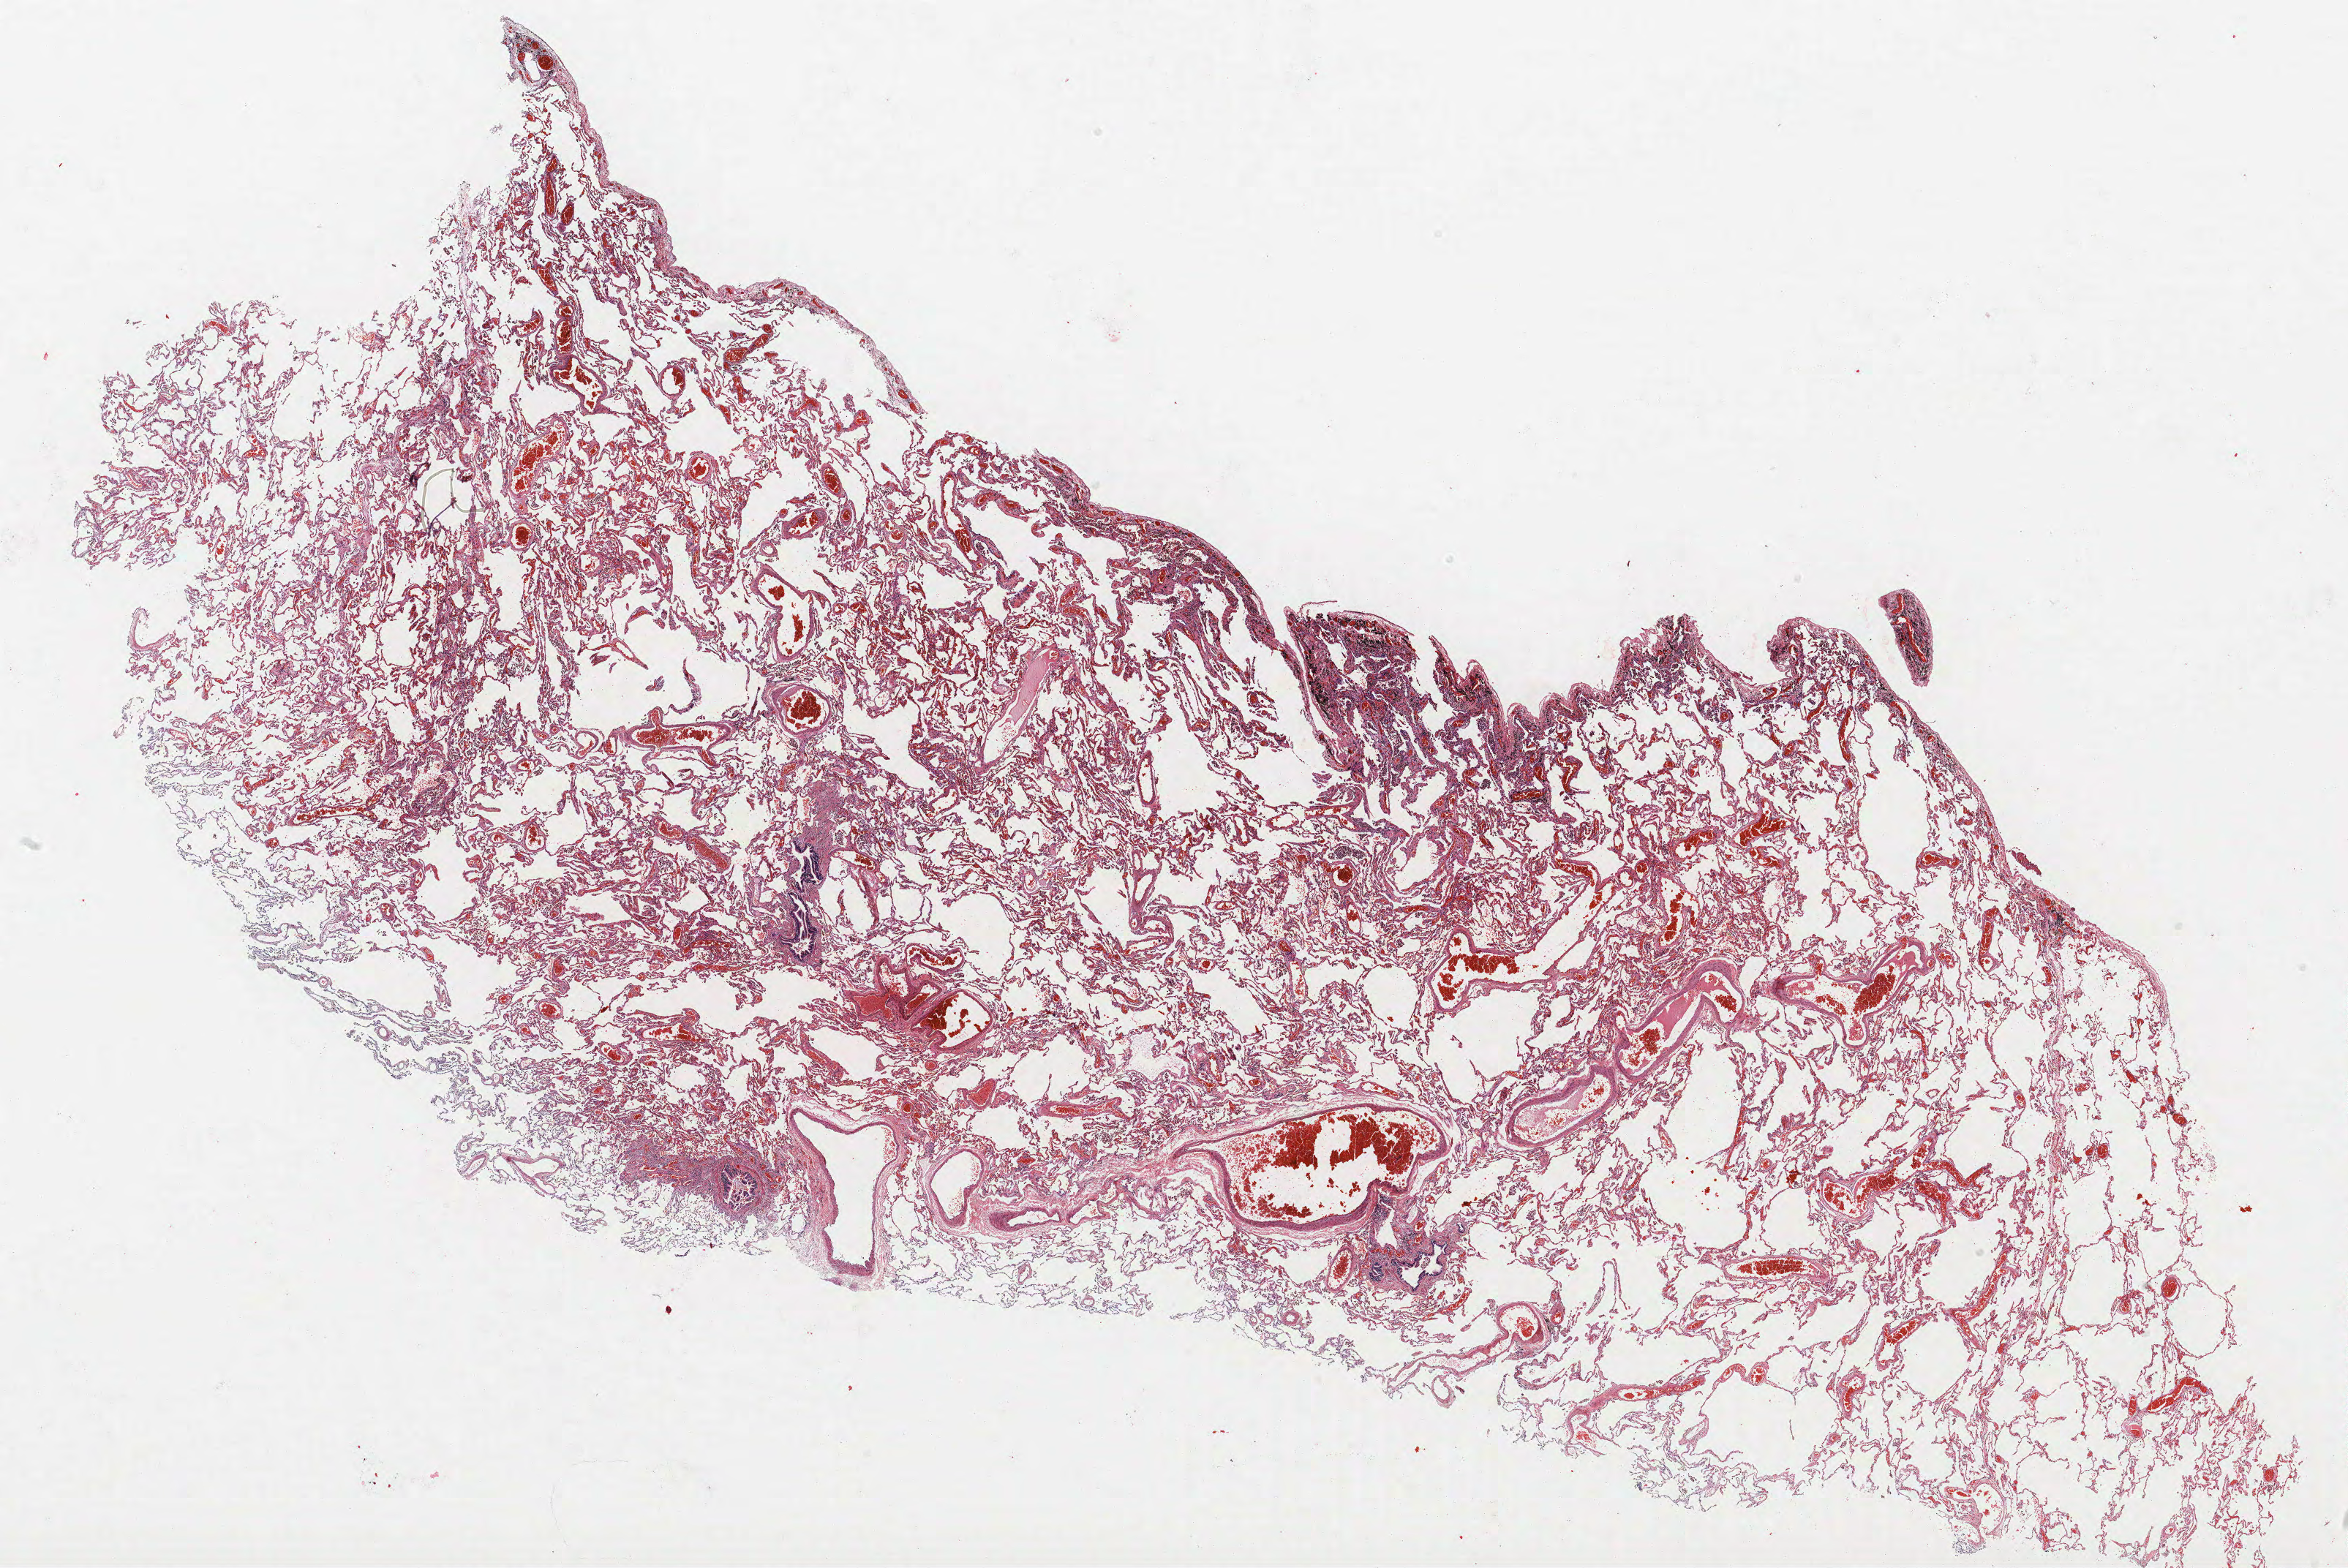
H&E whole-slide image, low-resolution overview of the scanned area, about 25.7 x 17.2 mm (acquisition: 40x scan); FFPE section; lung tissue. Male, age 69 at enrolment. Current smoker at enrolment. Grade: moderately differentiated (G2).
* stage (AJCC 6th edition): IB
* primary tumour location (clinical record): right upper lobe
* tumour size (pathology): 40 mm
* participant's lung-cancer diagnosis: Squamous cell carcinoma, NOS (ICD-O-3 8070/3)
* ICD-O-3 topography: upper lobe of lung (C34.1)